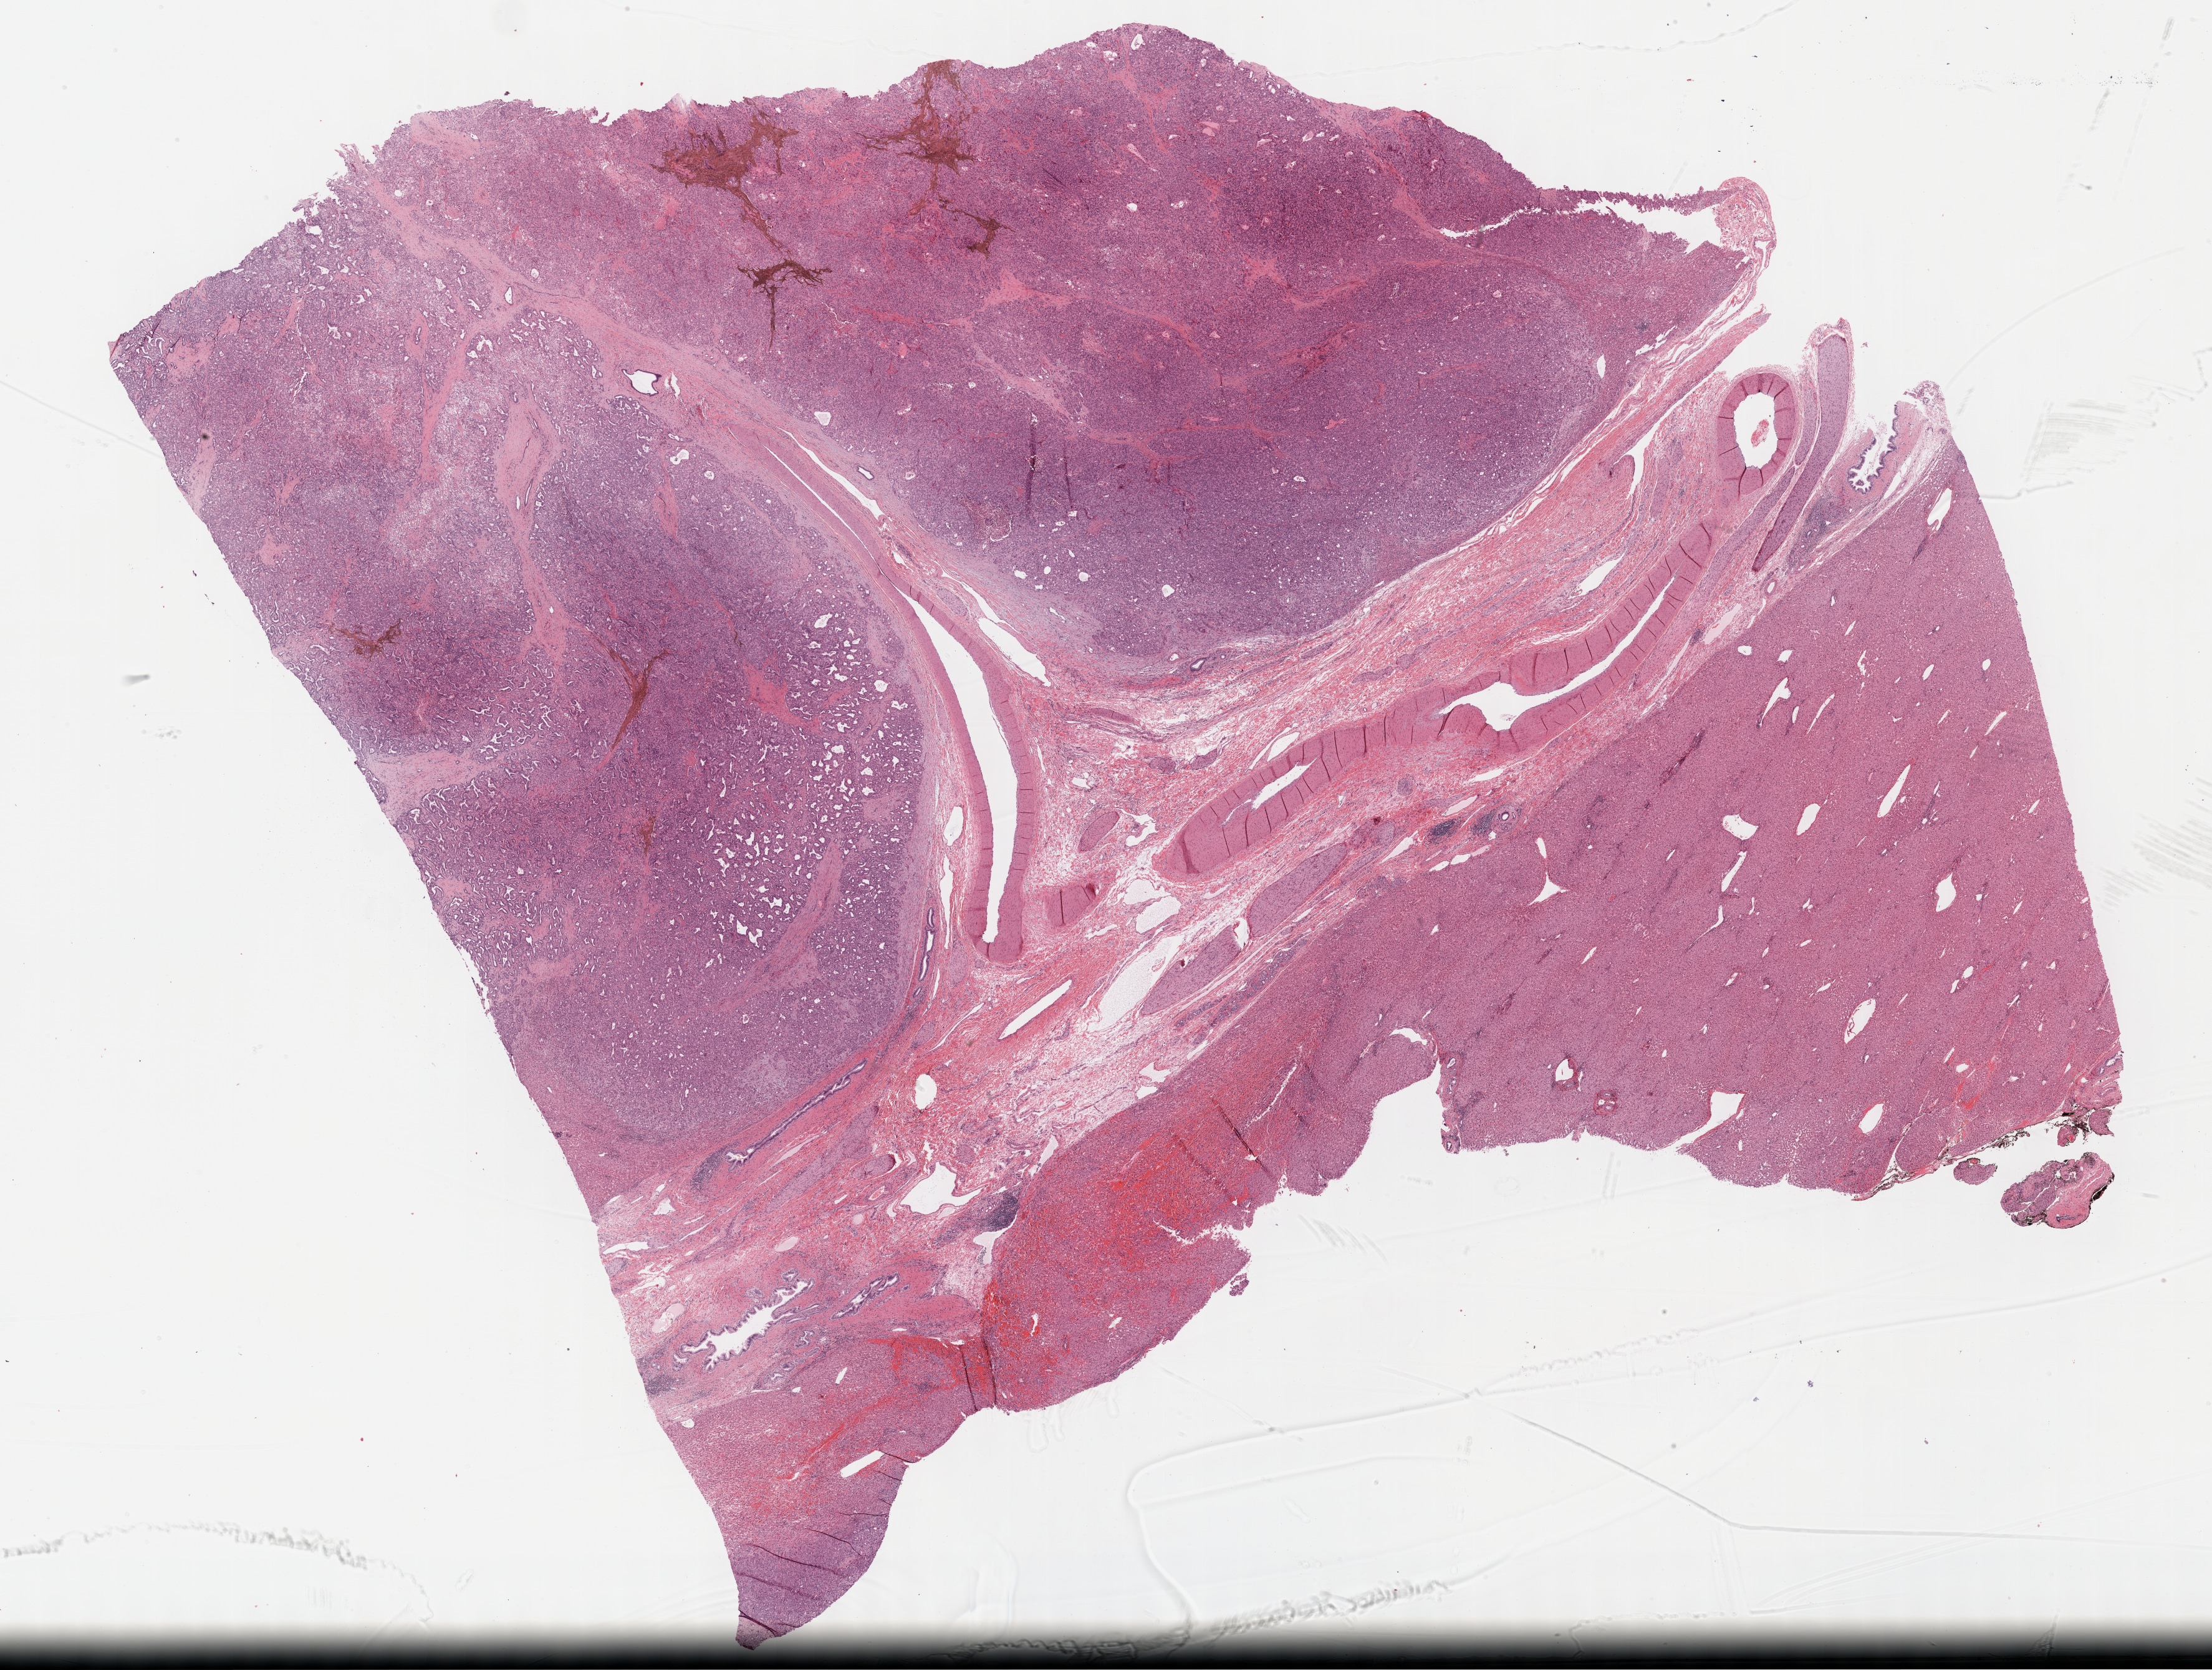
Digitized Hematoxylin and eosin (H&E) stained tissue section (whole slide) — shown as a low-resolution overview of the whole scanned area (about 28.7 x 21.7 mm, from a 40x scan), FFPE section, primary tumour sample from the liver. Patient: female, age at initial diagnosis 45 years. Histologic grade: G2 (moderately differentiated).
* AJCC pathologic stage: IIIA (6th edition)
* pathologic diagnosis: Hepatocellular carcinoma, NOS